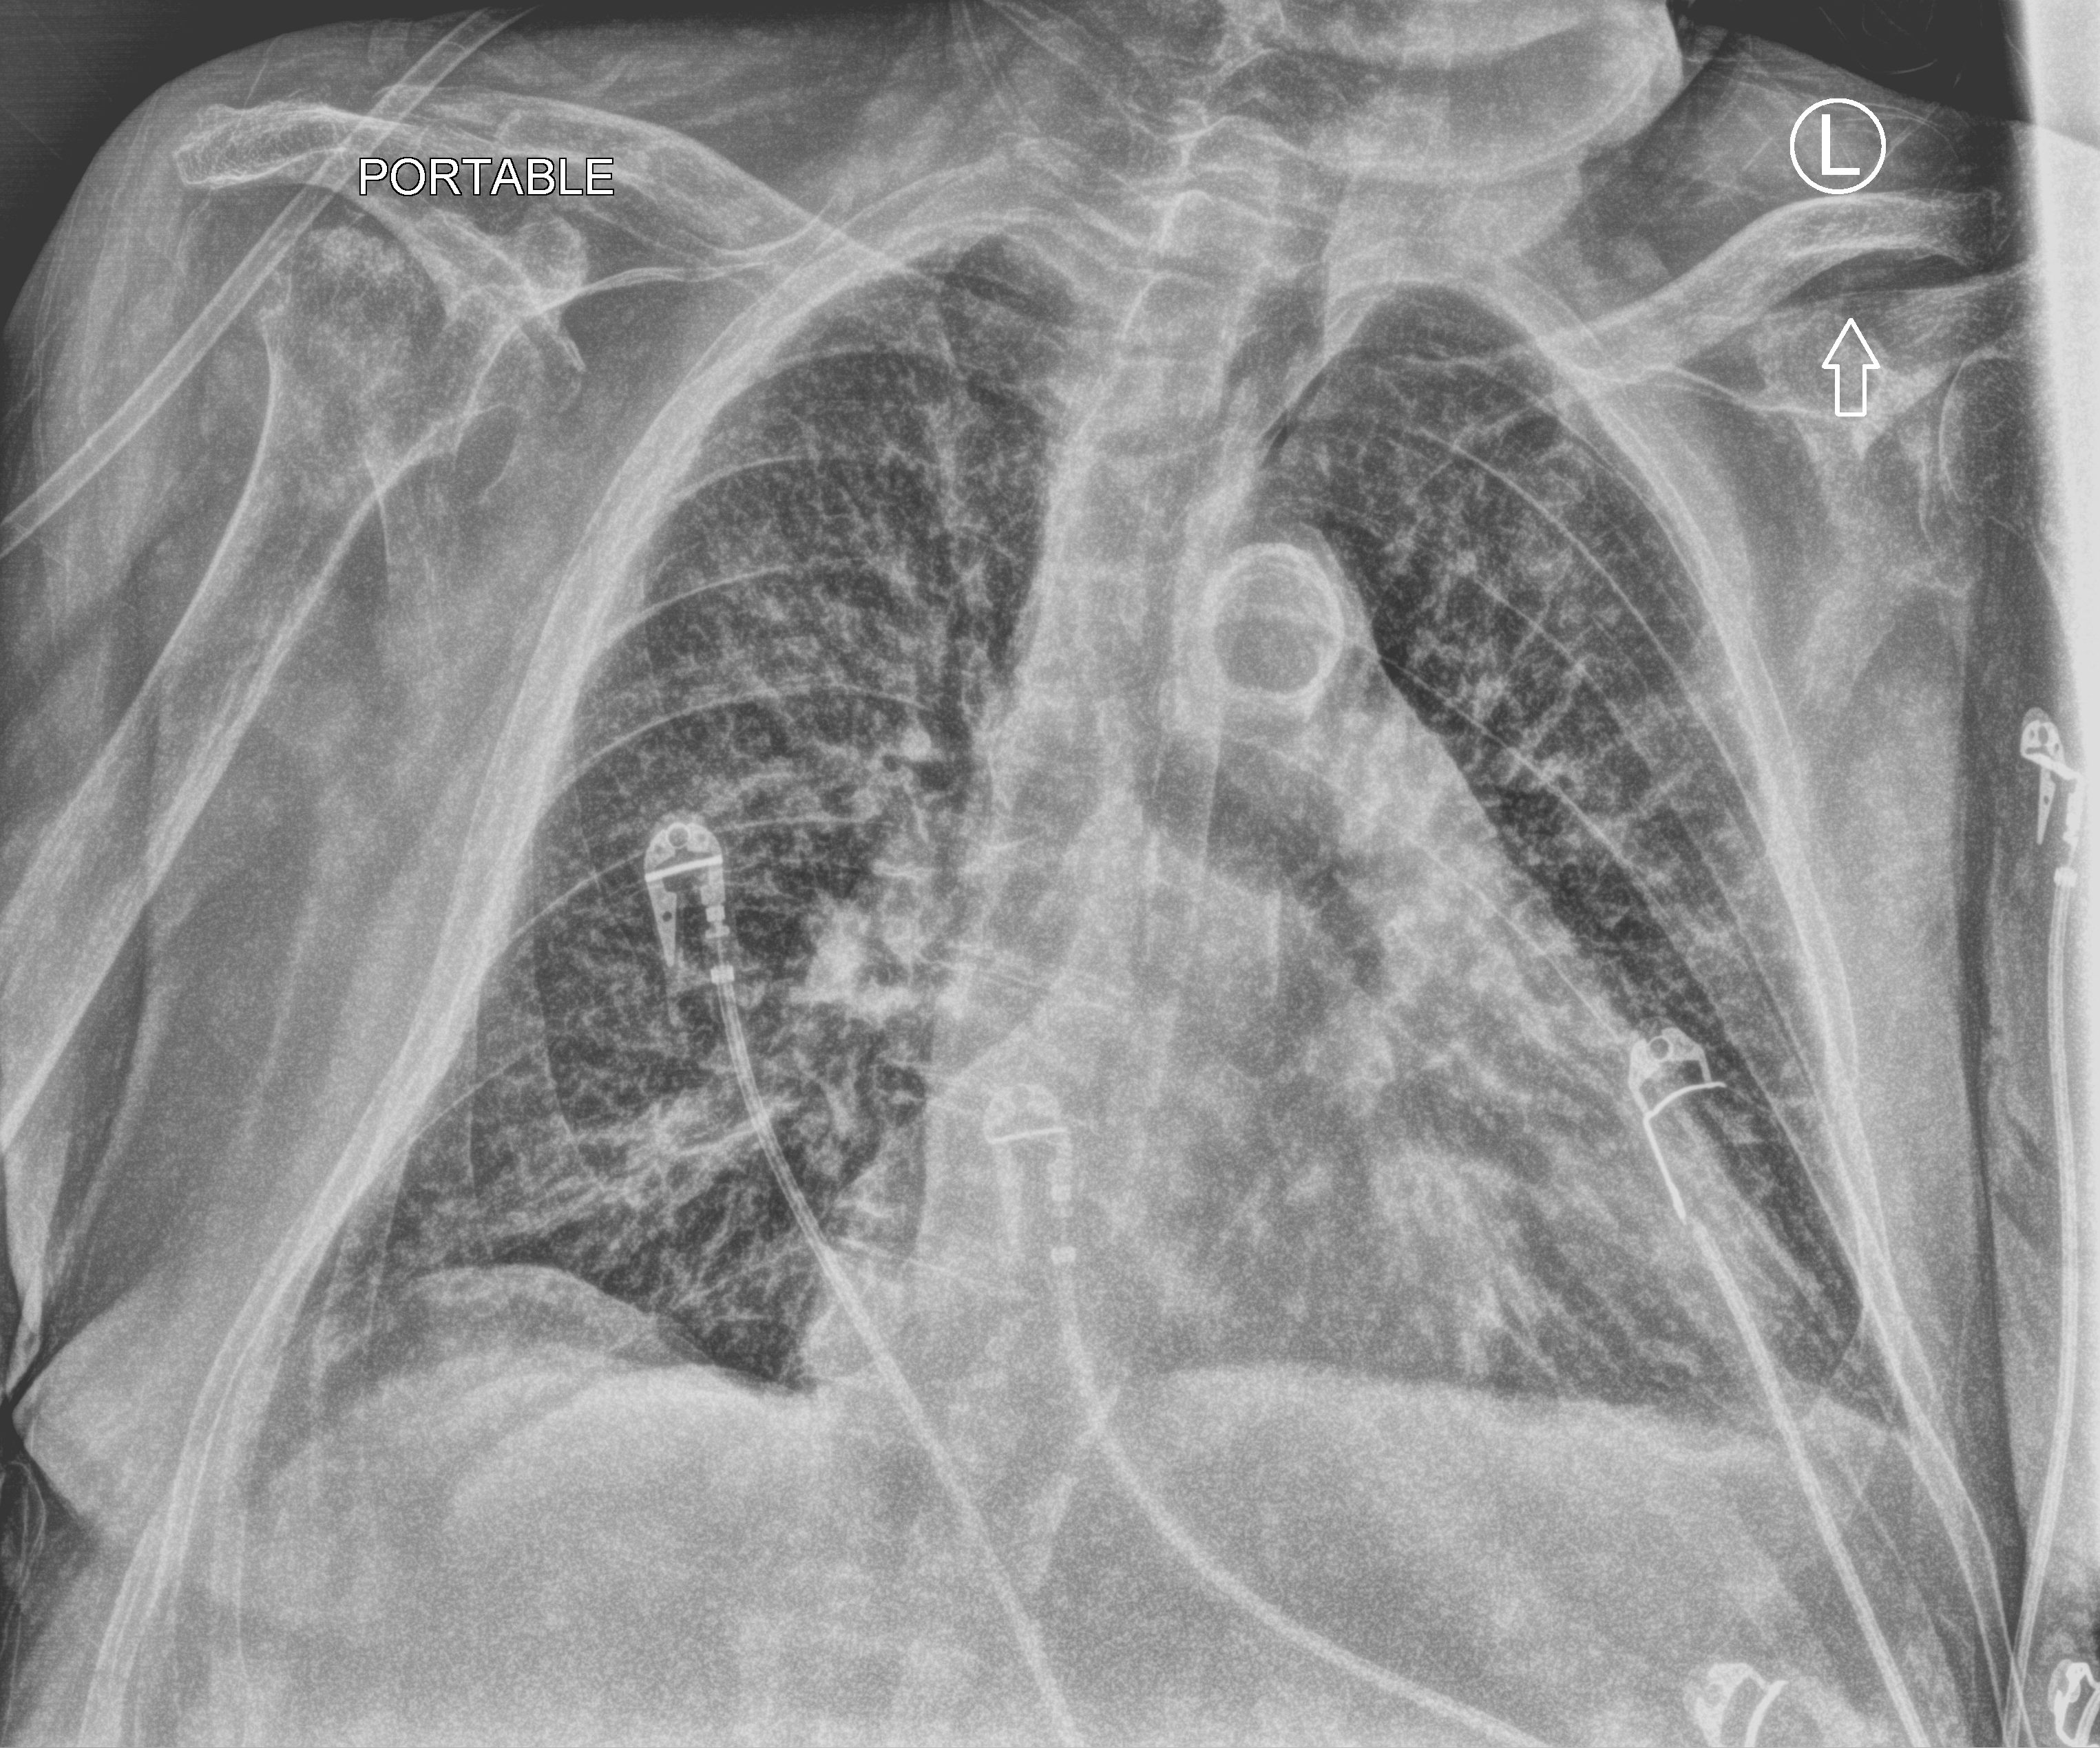
Portable chest radiograph; anteroposterior (AP) projection. Male patient hospitalised with COVID-19, age 75–90 years.
Admission-level facts for this patient (not findings on this image; timing relative to this image not recorded): mechanically ventilated during this hospital stay: no; hypertension (admission record): yes; length of hospital stay: 10 days.